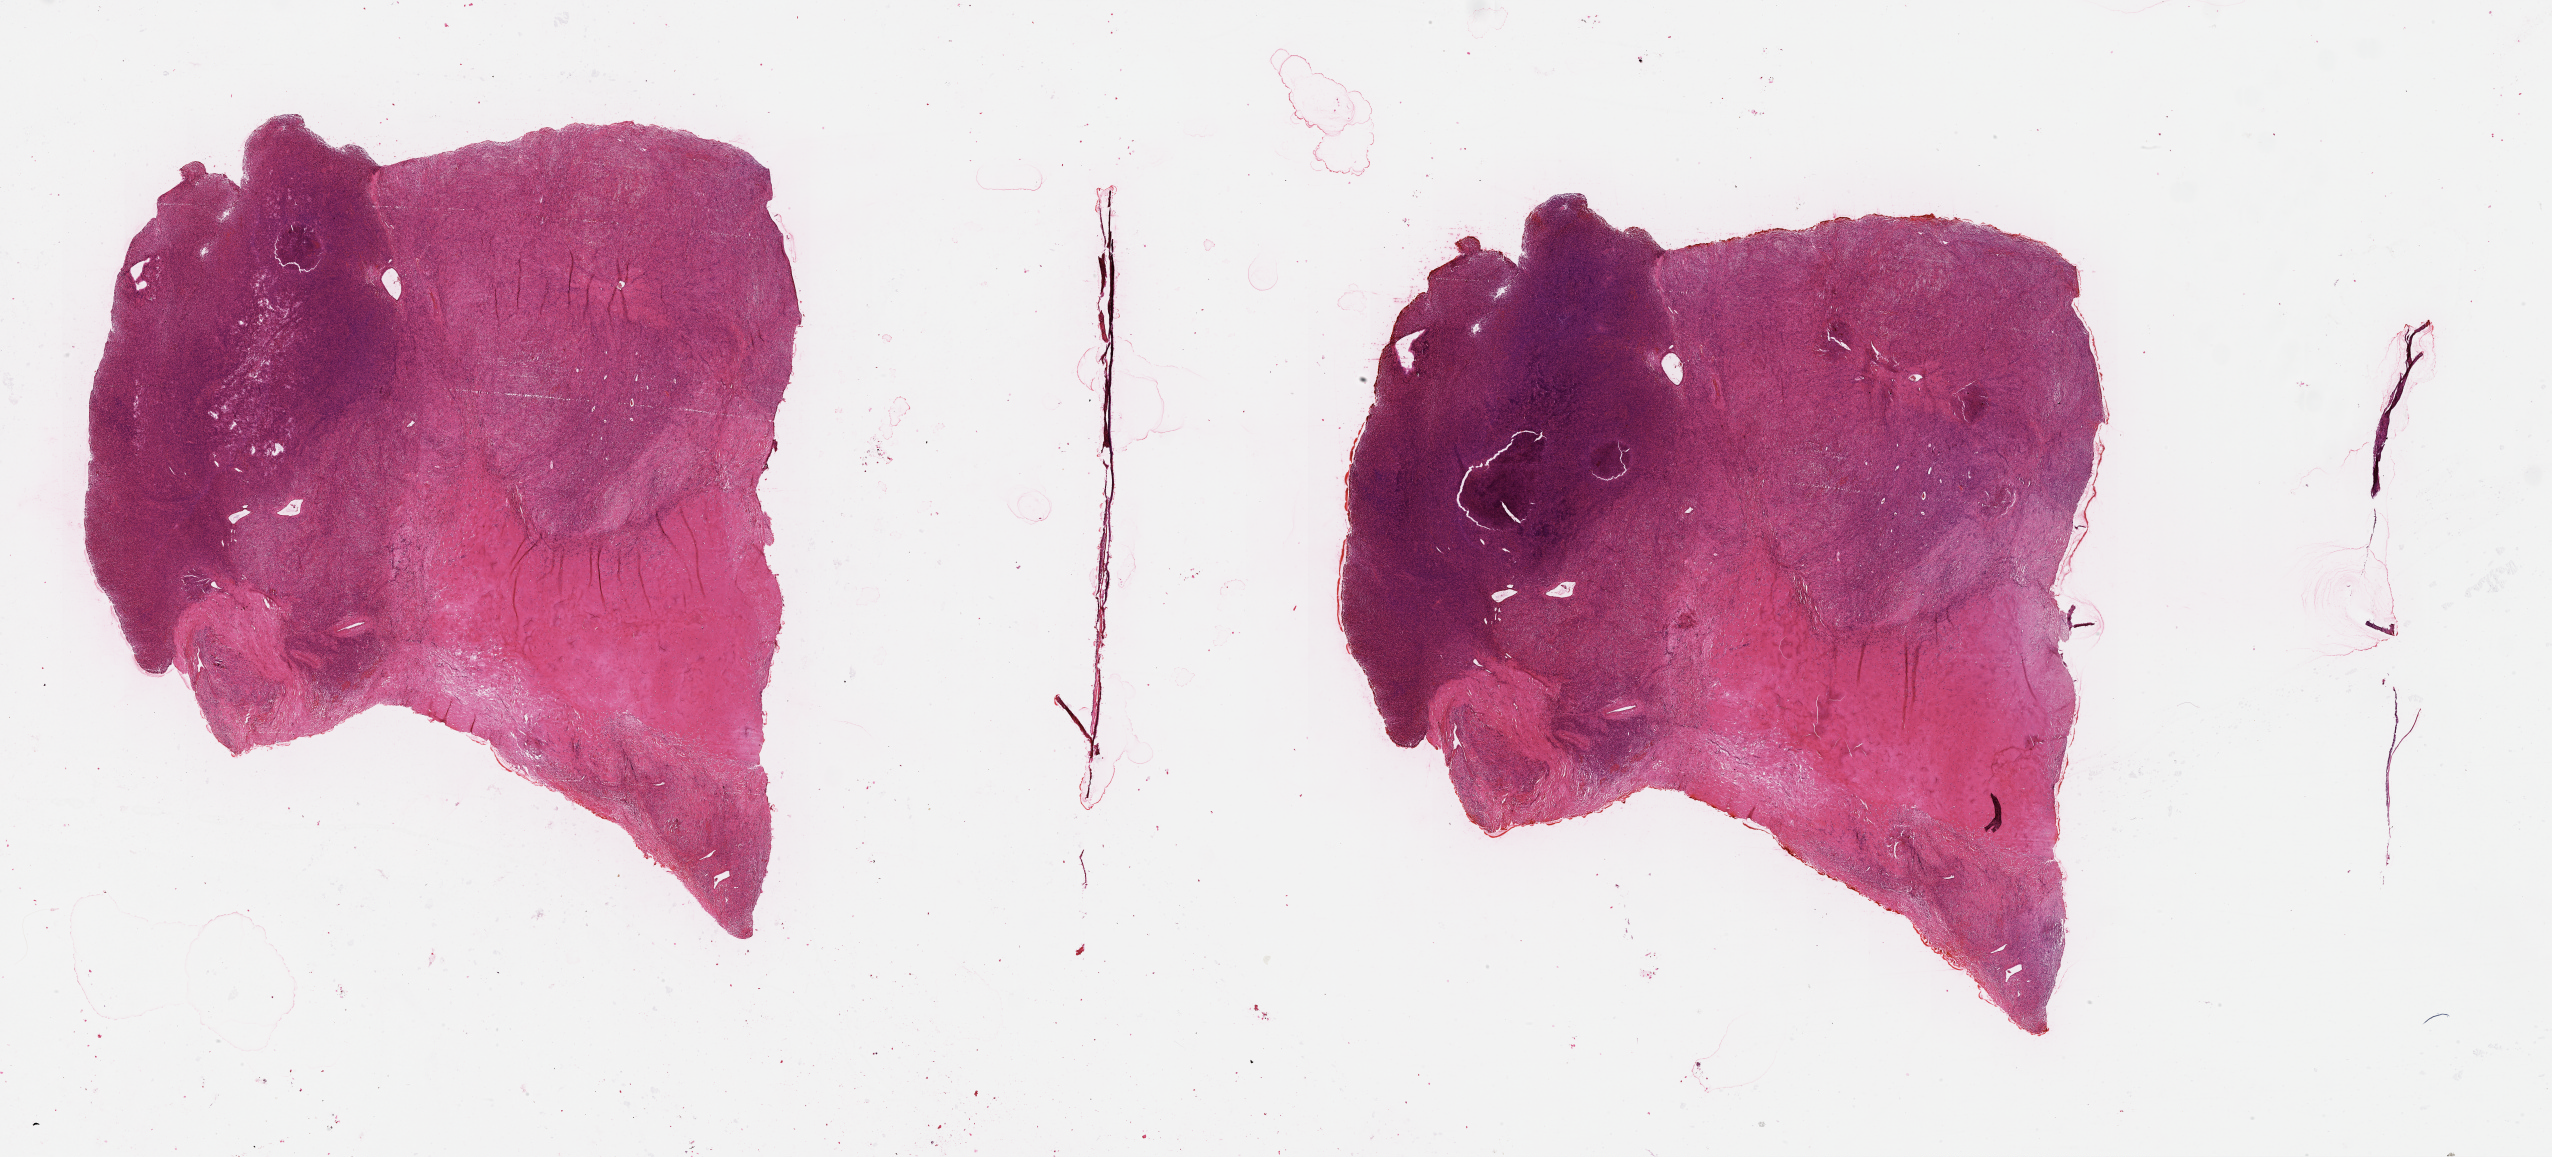
H&E whole-slide image — whole scanned area (about 41.1 x 18.6 mm, from a 20x scan) shown as a low-resolution overview, tumour tissue sample. Male, 62 y/o.
Patient diagnosis (cohort enrolment): sarcoma (site not recorded at cohort level). Primary tumour site (as recorded): chest.